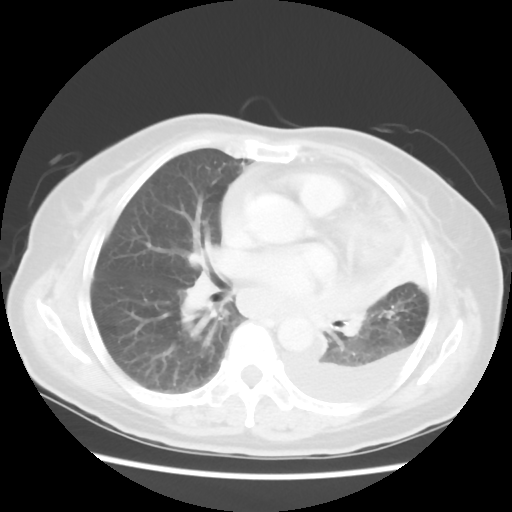
Chest CT, one axial slice. Position 29 of 52 along the scan axis. Reconstruction kernel STANDARD. 120 kVp. Lung window (W 1500 / L -600 HU). 5 mm slice thickness. 512 × 512 image matrix, field of view 336 × 336 mm. Patient: female, 72 years. From the clinical record (not read from this slice): clinical TNM (as recorded): T4 N3 M1b.
Outlined on this slice (rectangle marked by the reading radiologist):
- lung tumour (recorded histology: large cell carcinoma): bounding box [x1, y1, x2, y2] px = [311, 276, 382, 338]